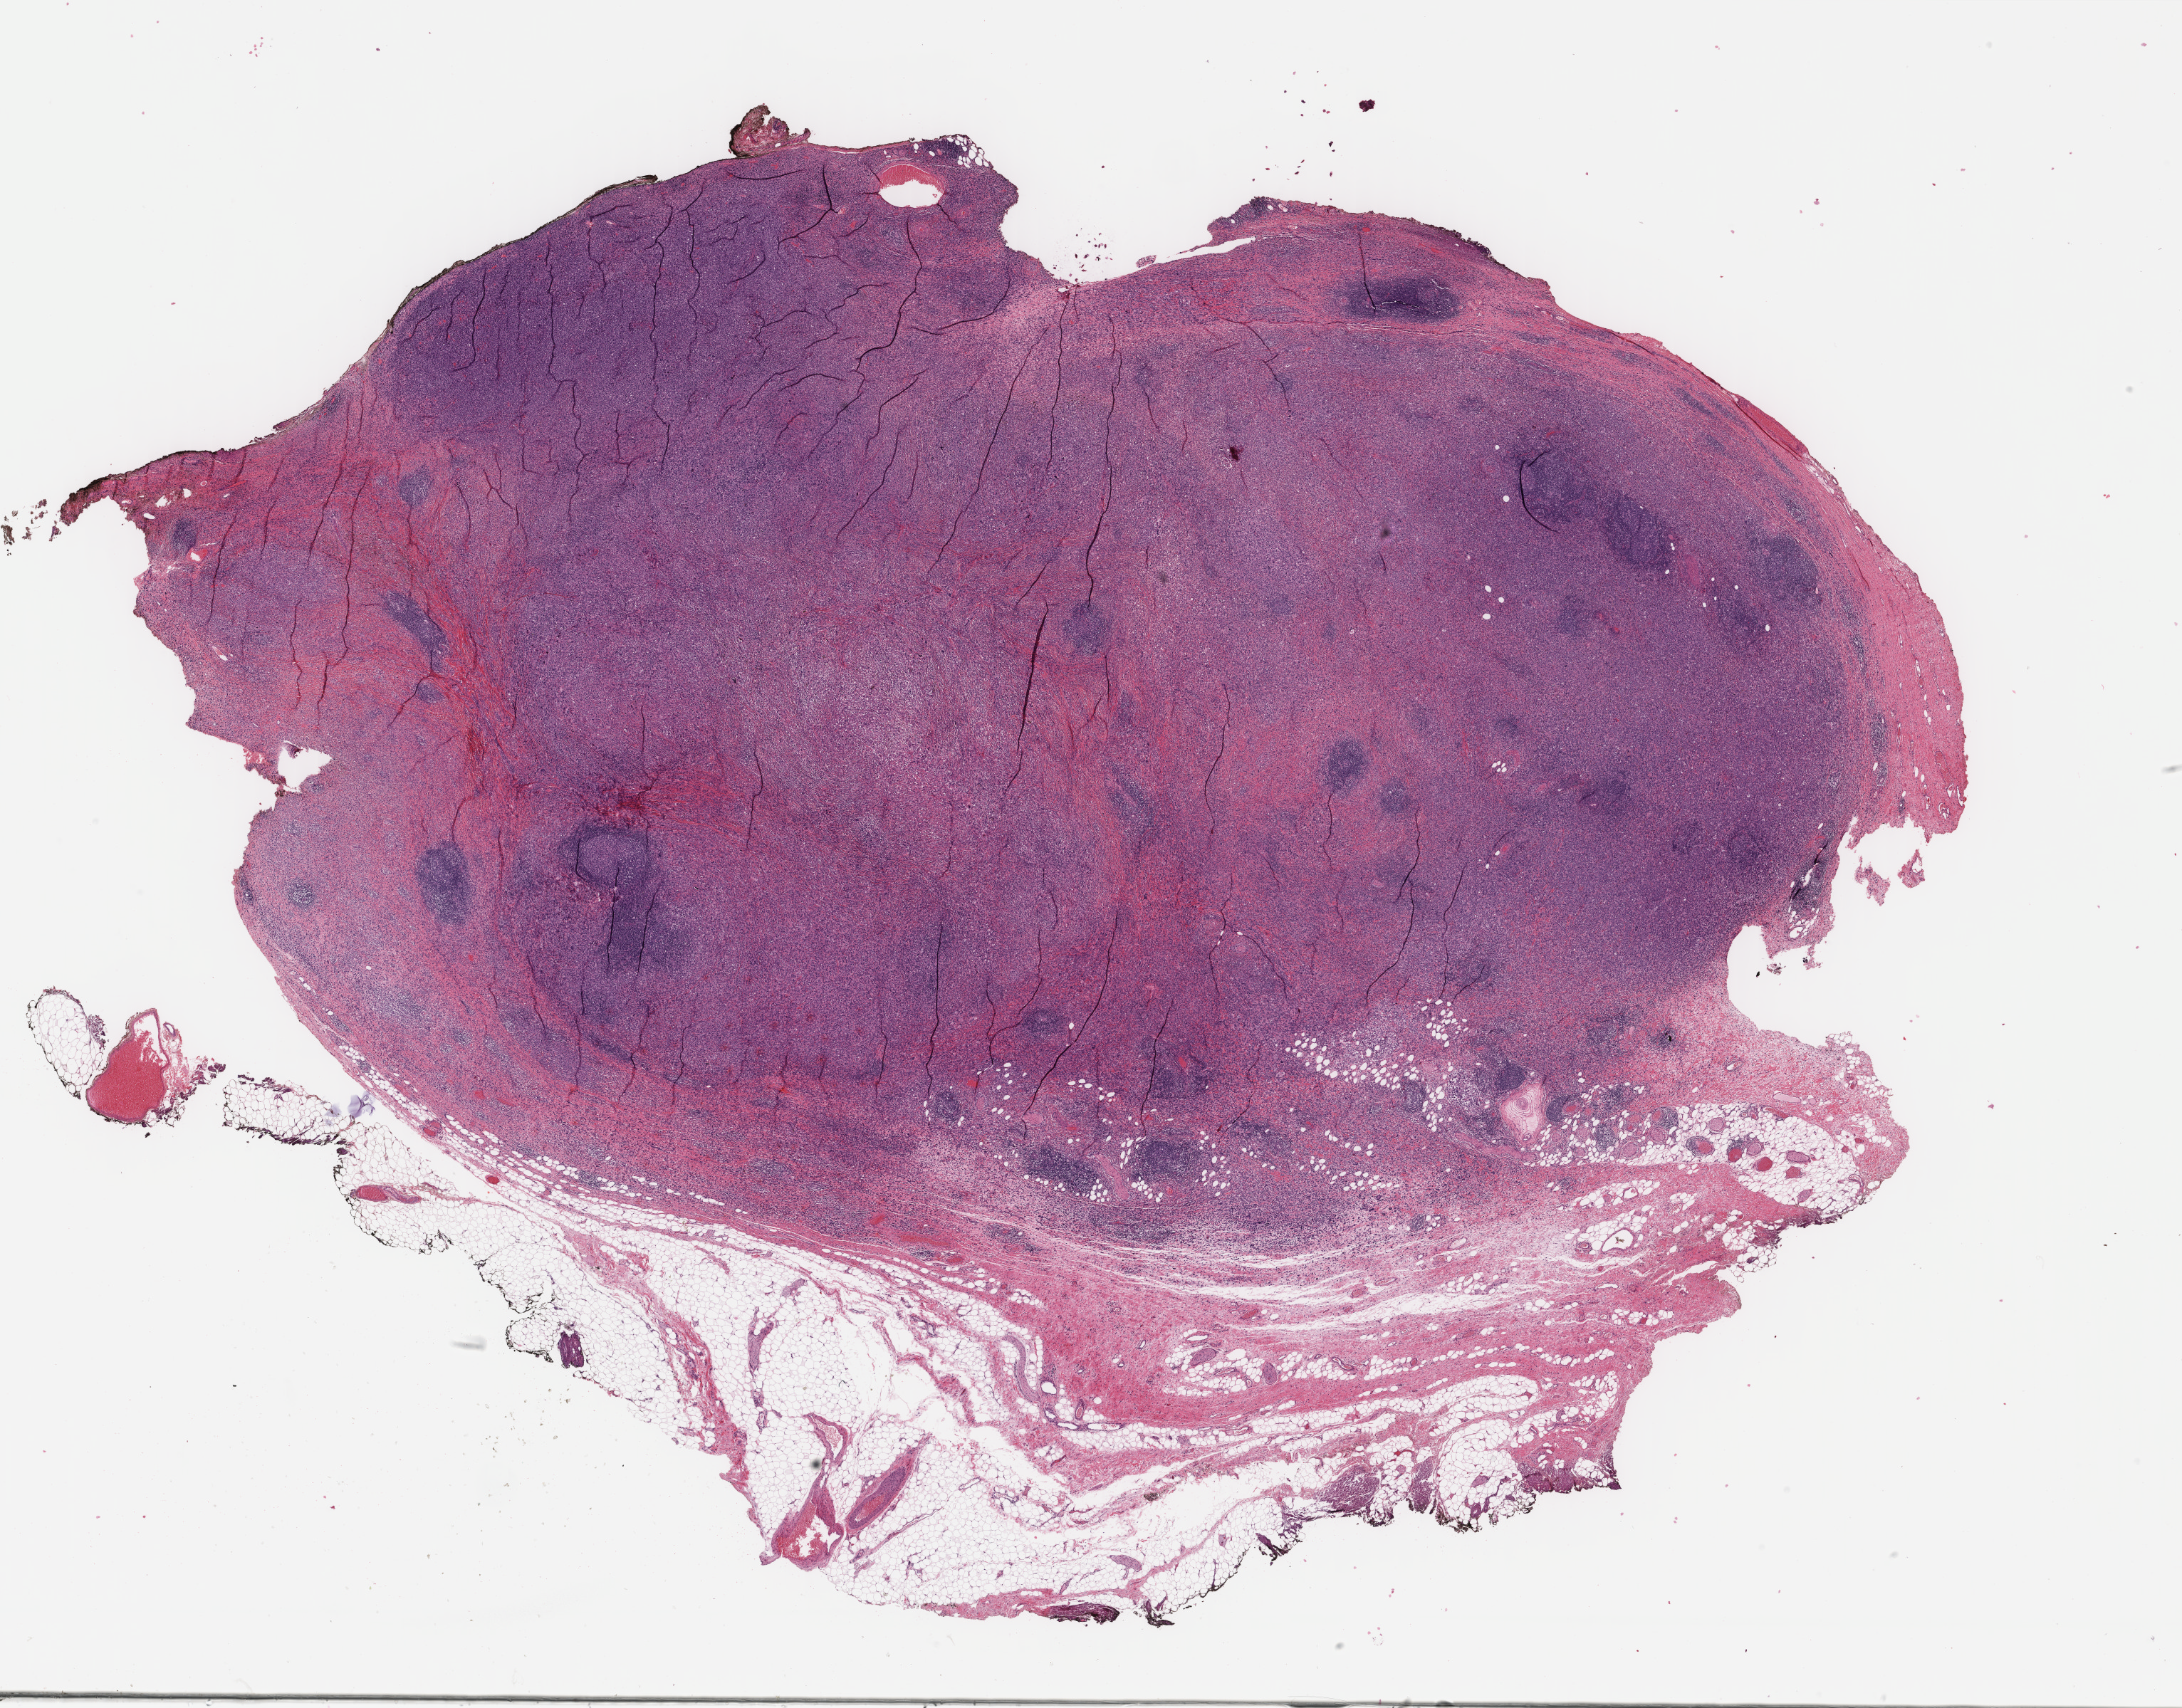
Whole-slide histology image, Hematoxylin and eosin (H&E) stained — a low-resolution overview of the entire scanned area, about 24.3 x 19.0 mm. Formalin-fixed paraffin-embedded (FFPE) diagnostic section. Metastatic tumour sample. Female patient; age at initial diagnosis 64 years.
This section: metastatic tumour tissue. Patient diagnosis: Malignant melanoma, NOS.